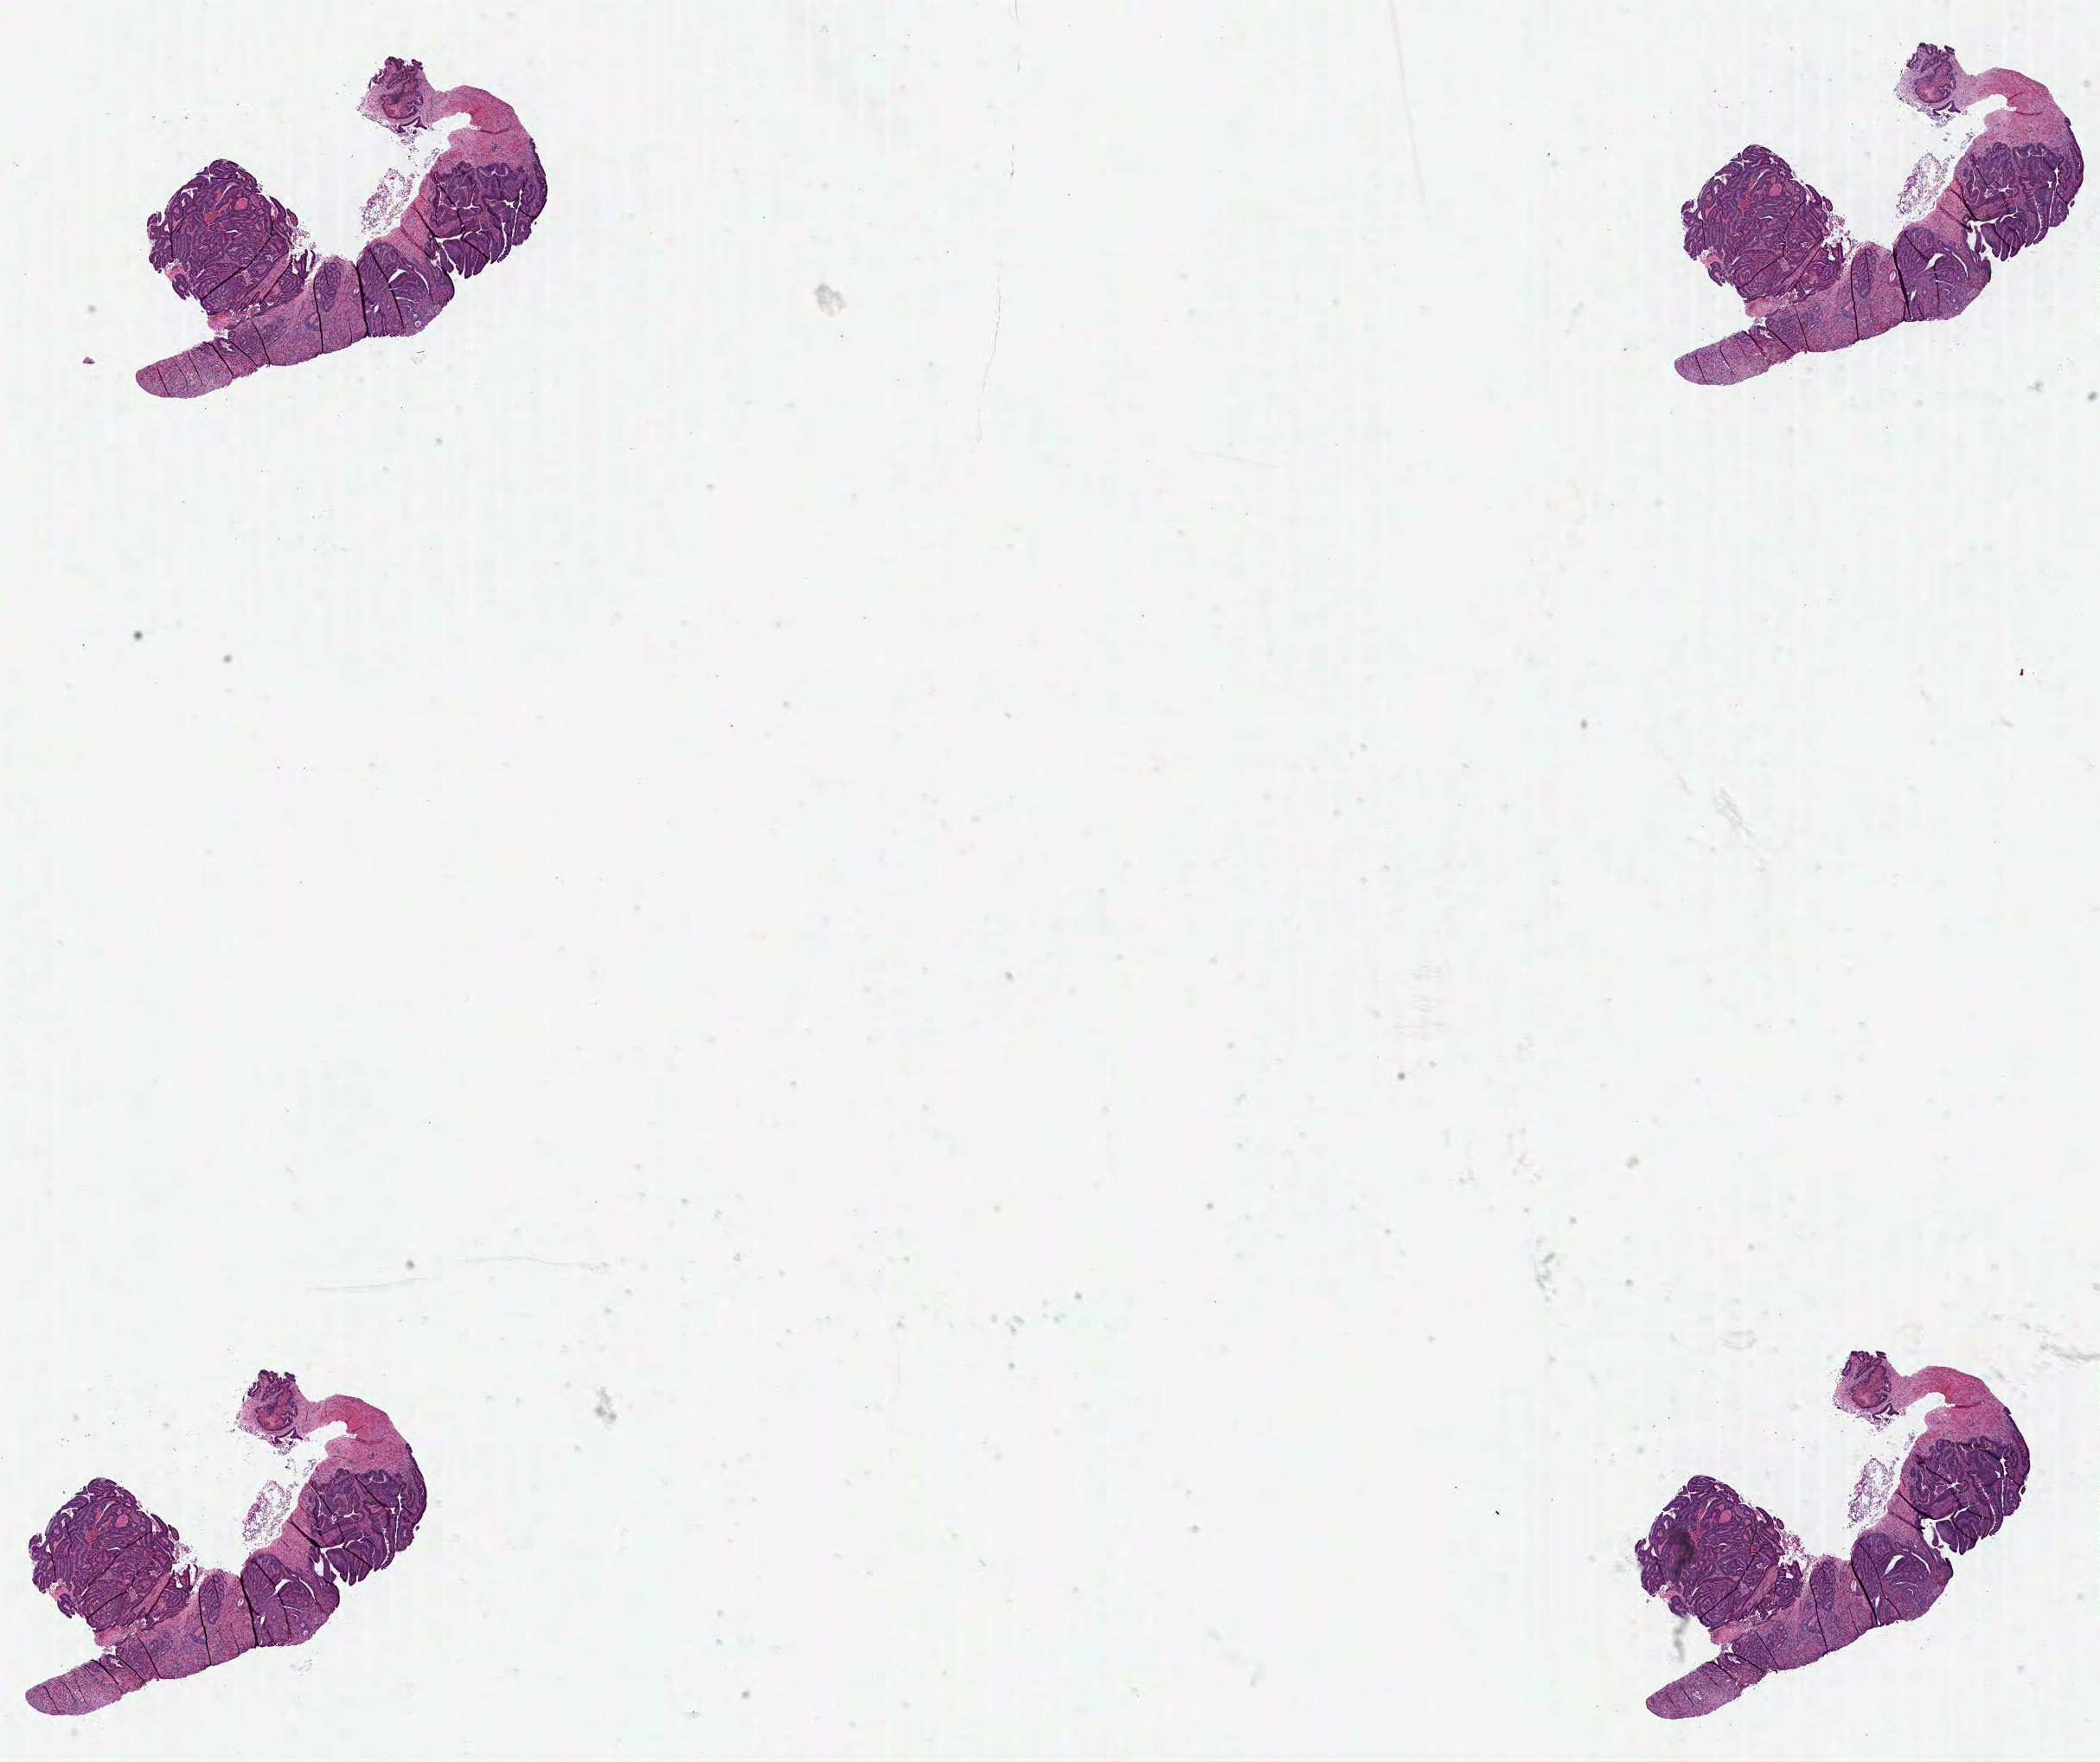
H&E-stained whole-slide image, low-resolution overview of the scanned area, about 19.6 x 16.4 mm (slide scanned at 40x), FFPE section, sample: primary tumour, colon. Patient: male, age at initial diagnosis 59 years.
AJCC pathologic stage: IVA. TNM: T3 N0 M1. Diagnosis: Adenocarcinoma, NOS. Lymph nodes positive (case pathology): 0 of 22 examined.